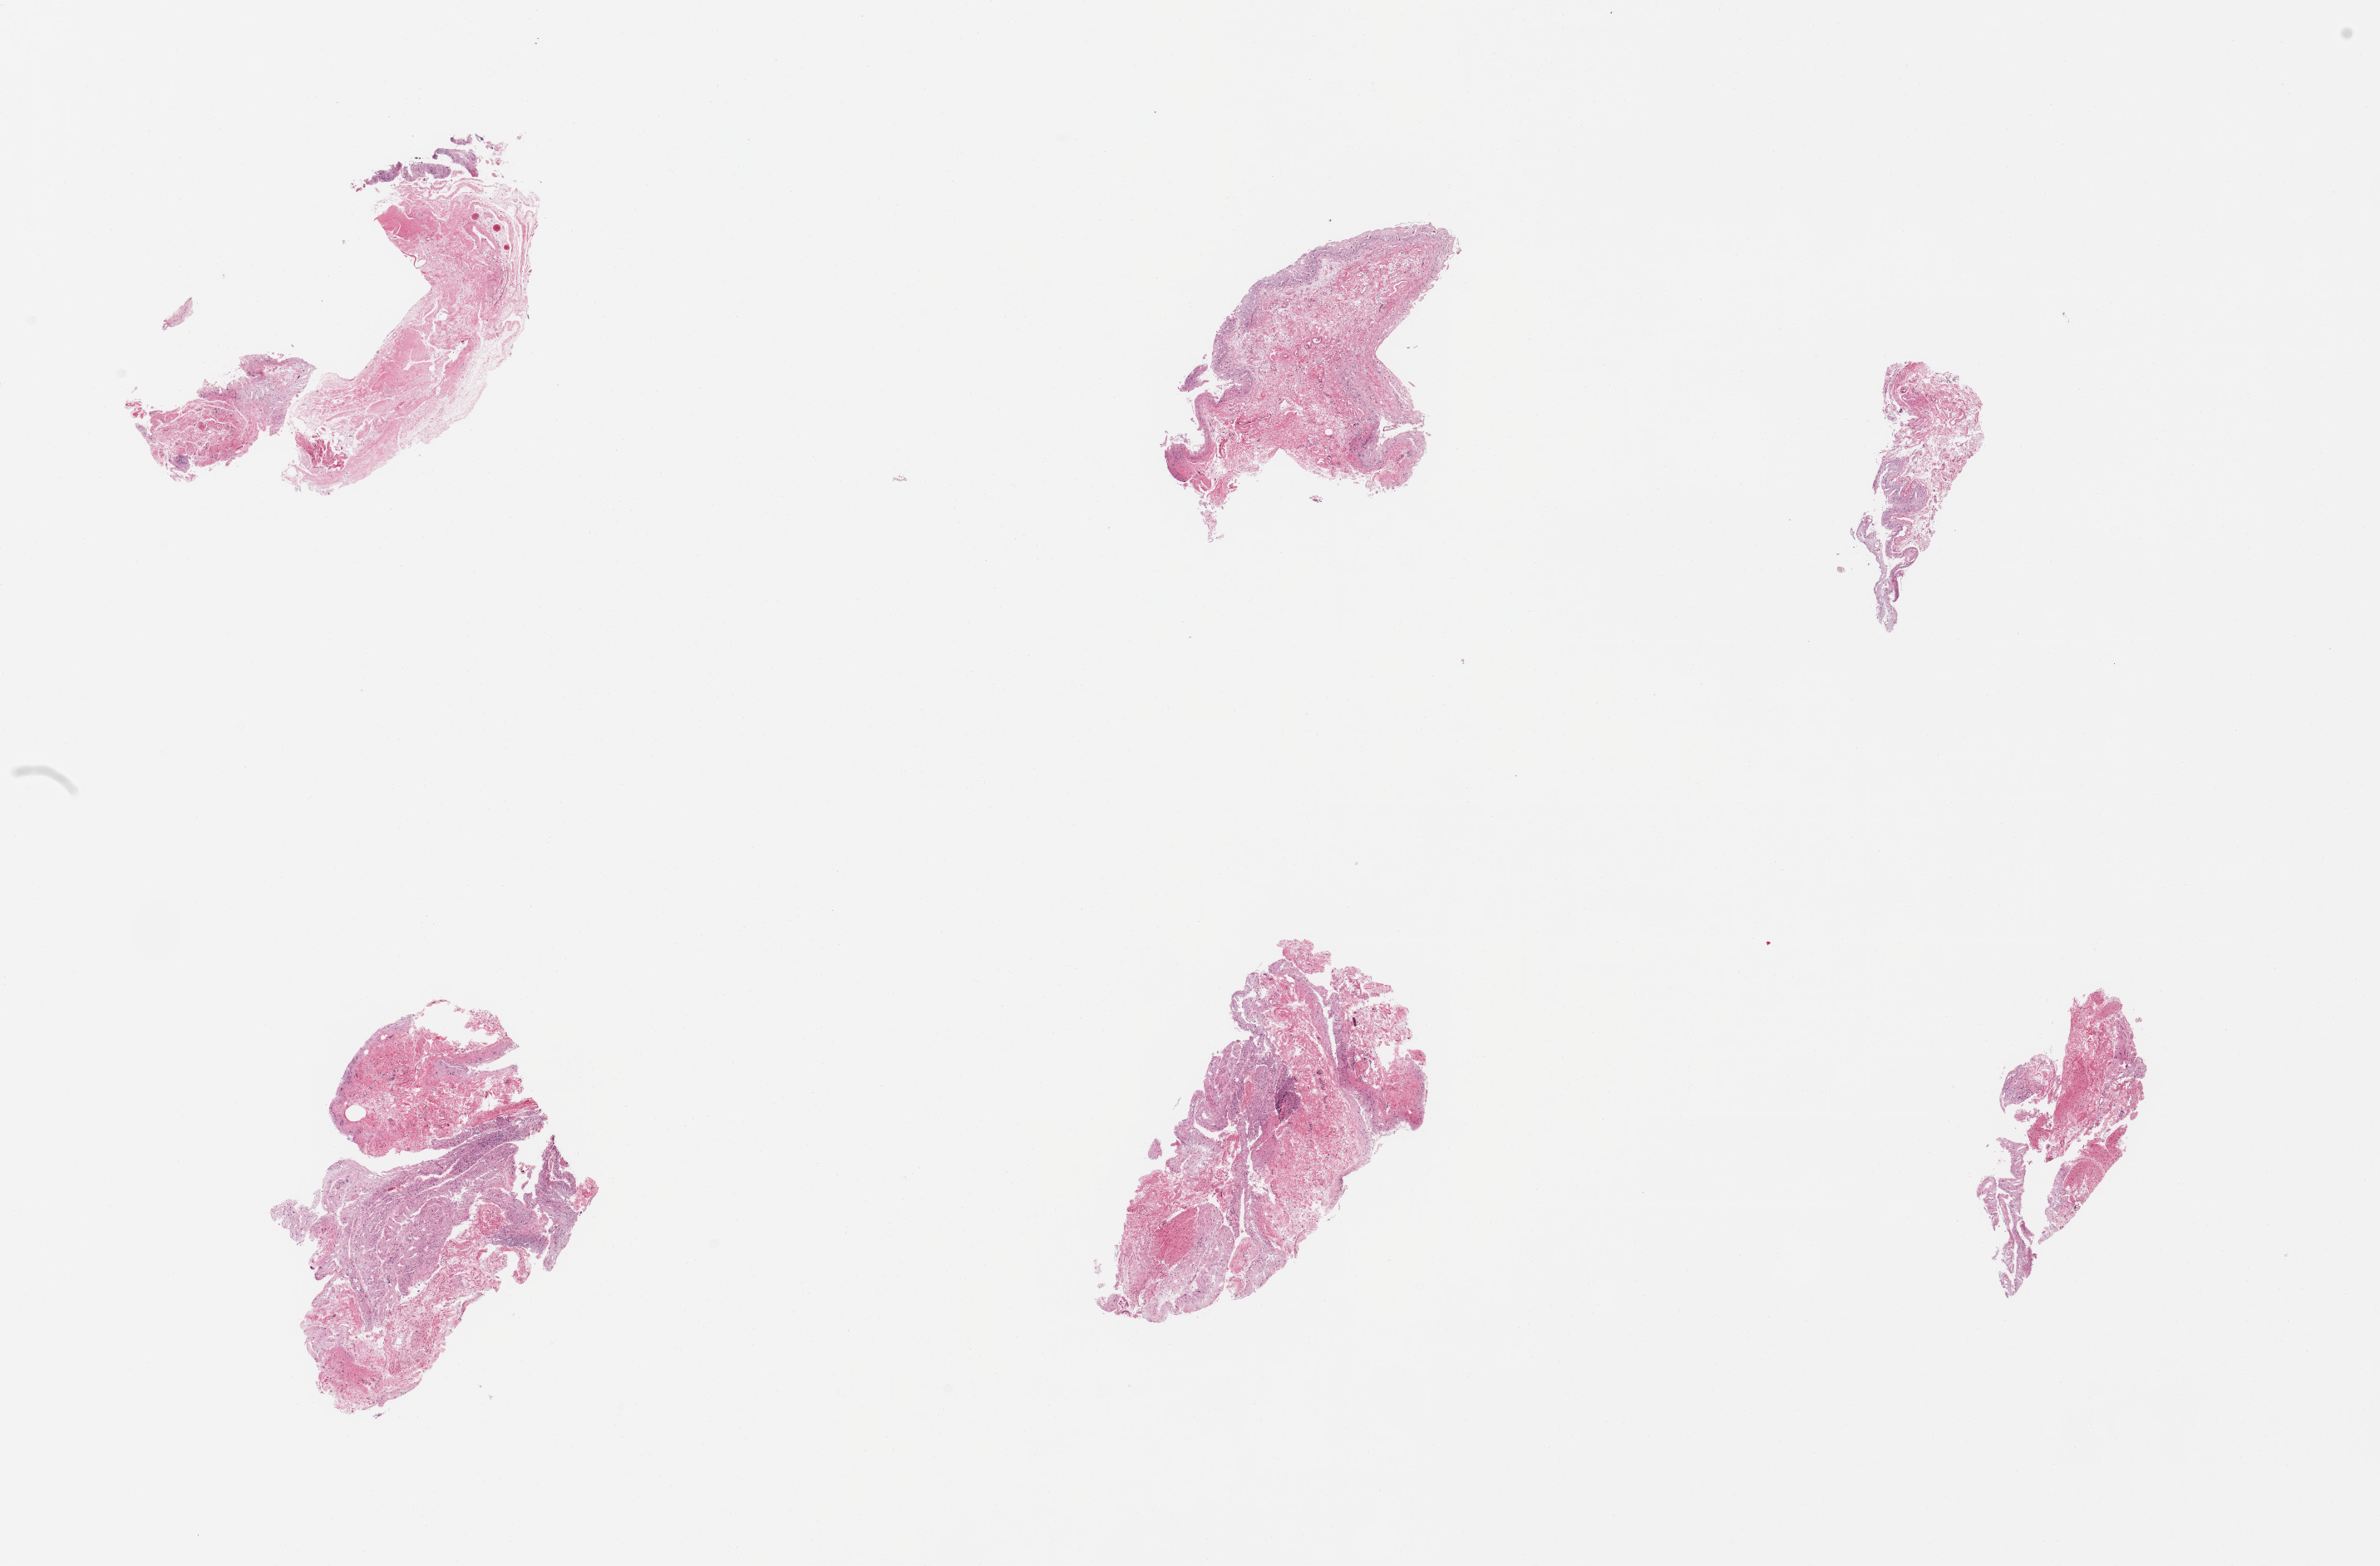
Haematoxylin and eosin whole-slide image, brightfield, shown as a low-resolution overview of the whole scanned area (about 22.6 x 14.9 mm, slide scanned at 20x); PAXgene-fixed, paraffin-embedded tissue; sampled site (target tissue): ileum; tissue donor sample. Donor: female.
Review note (as recorded): 6 pieces; autolyzed and without lymphoid tissue.